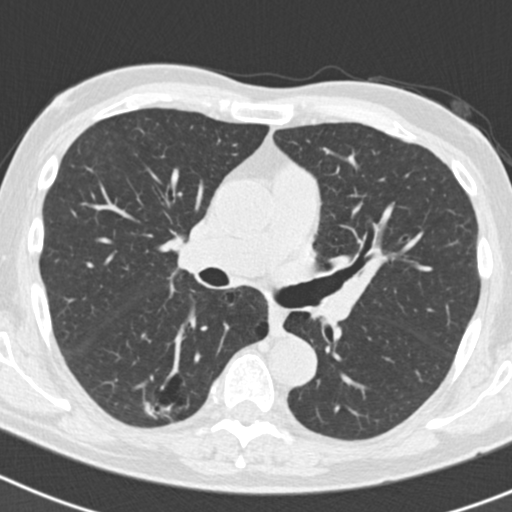
Chest CT (low-dose screening protocol), one axial image; second annual screen; lung window (W 1500 / L -600 HU); 2 mm slice thickness; slice 75 of 186 in the series; 512 × 512 image matrix. Male participant, aged 70 years at enrolment. Current smoker at enrolment.
- Lesion marked by an expert reader, bounding box <133,376,197,433> (left, top, right, bottom; pixels).
- The screening reader recorded 5 non-calcified nodules or masses ≥4 mm on this exam (right lower lobe, right lower lobe, right upper lobe, right upper lobe, left upper lobe); which of them this box marks is not recorded.
- Lung cancer was diagnosed 622 days after this screen (after the third annual screen): bronchiolo-alveolar adenocarcinoma, NOS, right lower lobe, poorly differentiated (G3), stage IB (AJCC 6th edition), 30 mm at pathology.